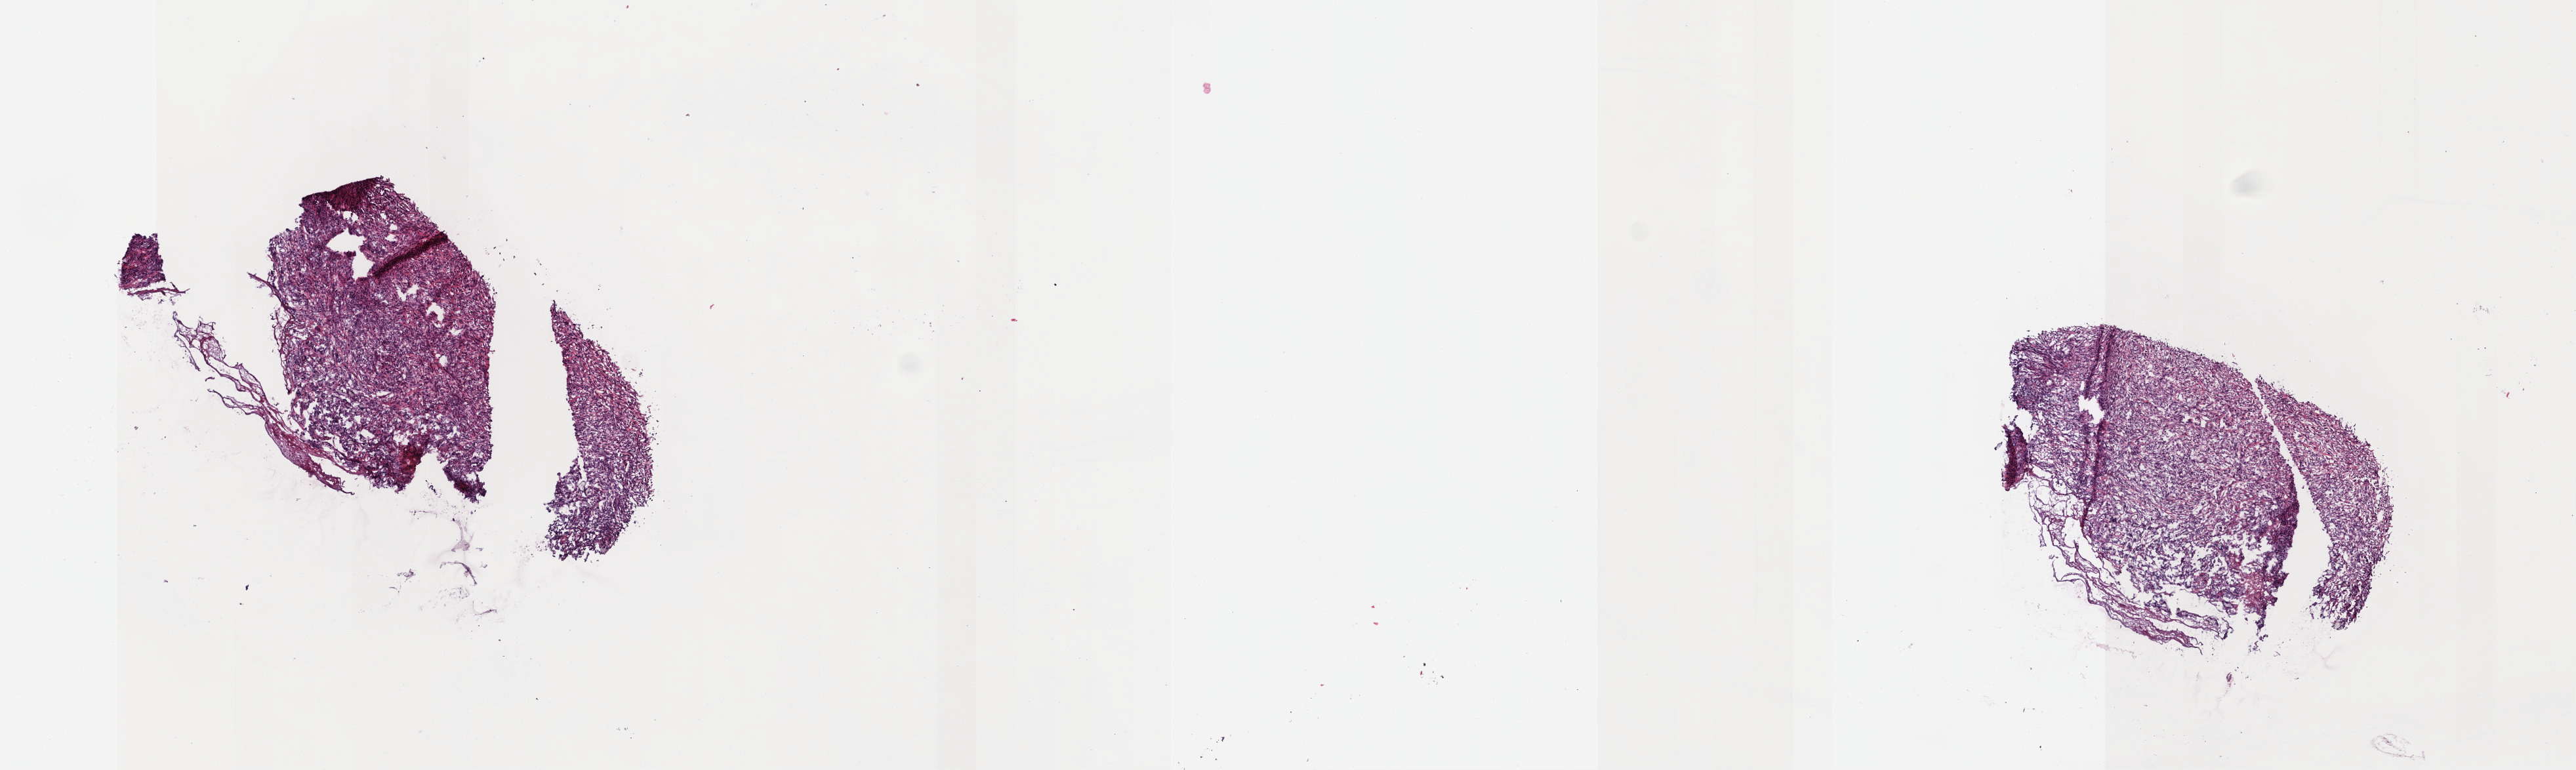
Hematoxylin and eosin (H&E) stained whole-slide image, a low-resolution overview of the entire scanned area, about 15.4 x 4.6 mm (acquisition: 40x scan). Frozen section from the top of the tissue portion. Mesothelium, primary tumour sample. Male patient; age at initial diagnosis 81 years. Composition of this section per pathologist review: tumour cells 100%, tumour nuclei 90%.
Pathologic diagnosis: Mesothelioma, malignant (pleura, NOS).